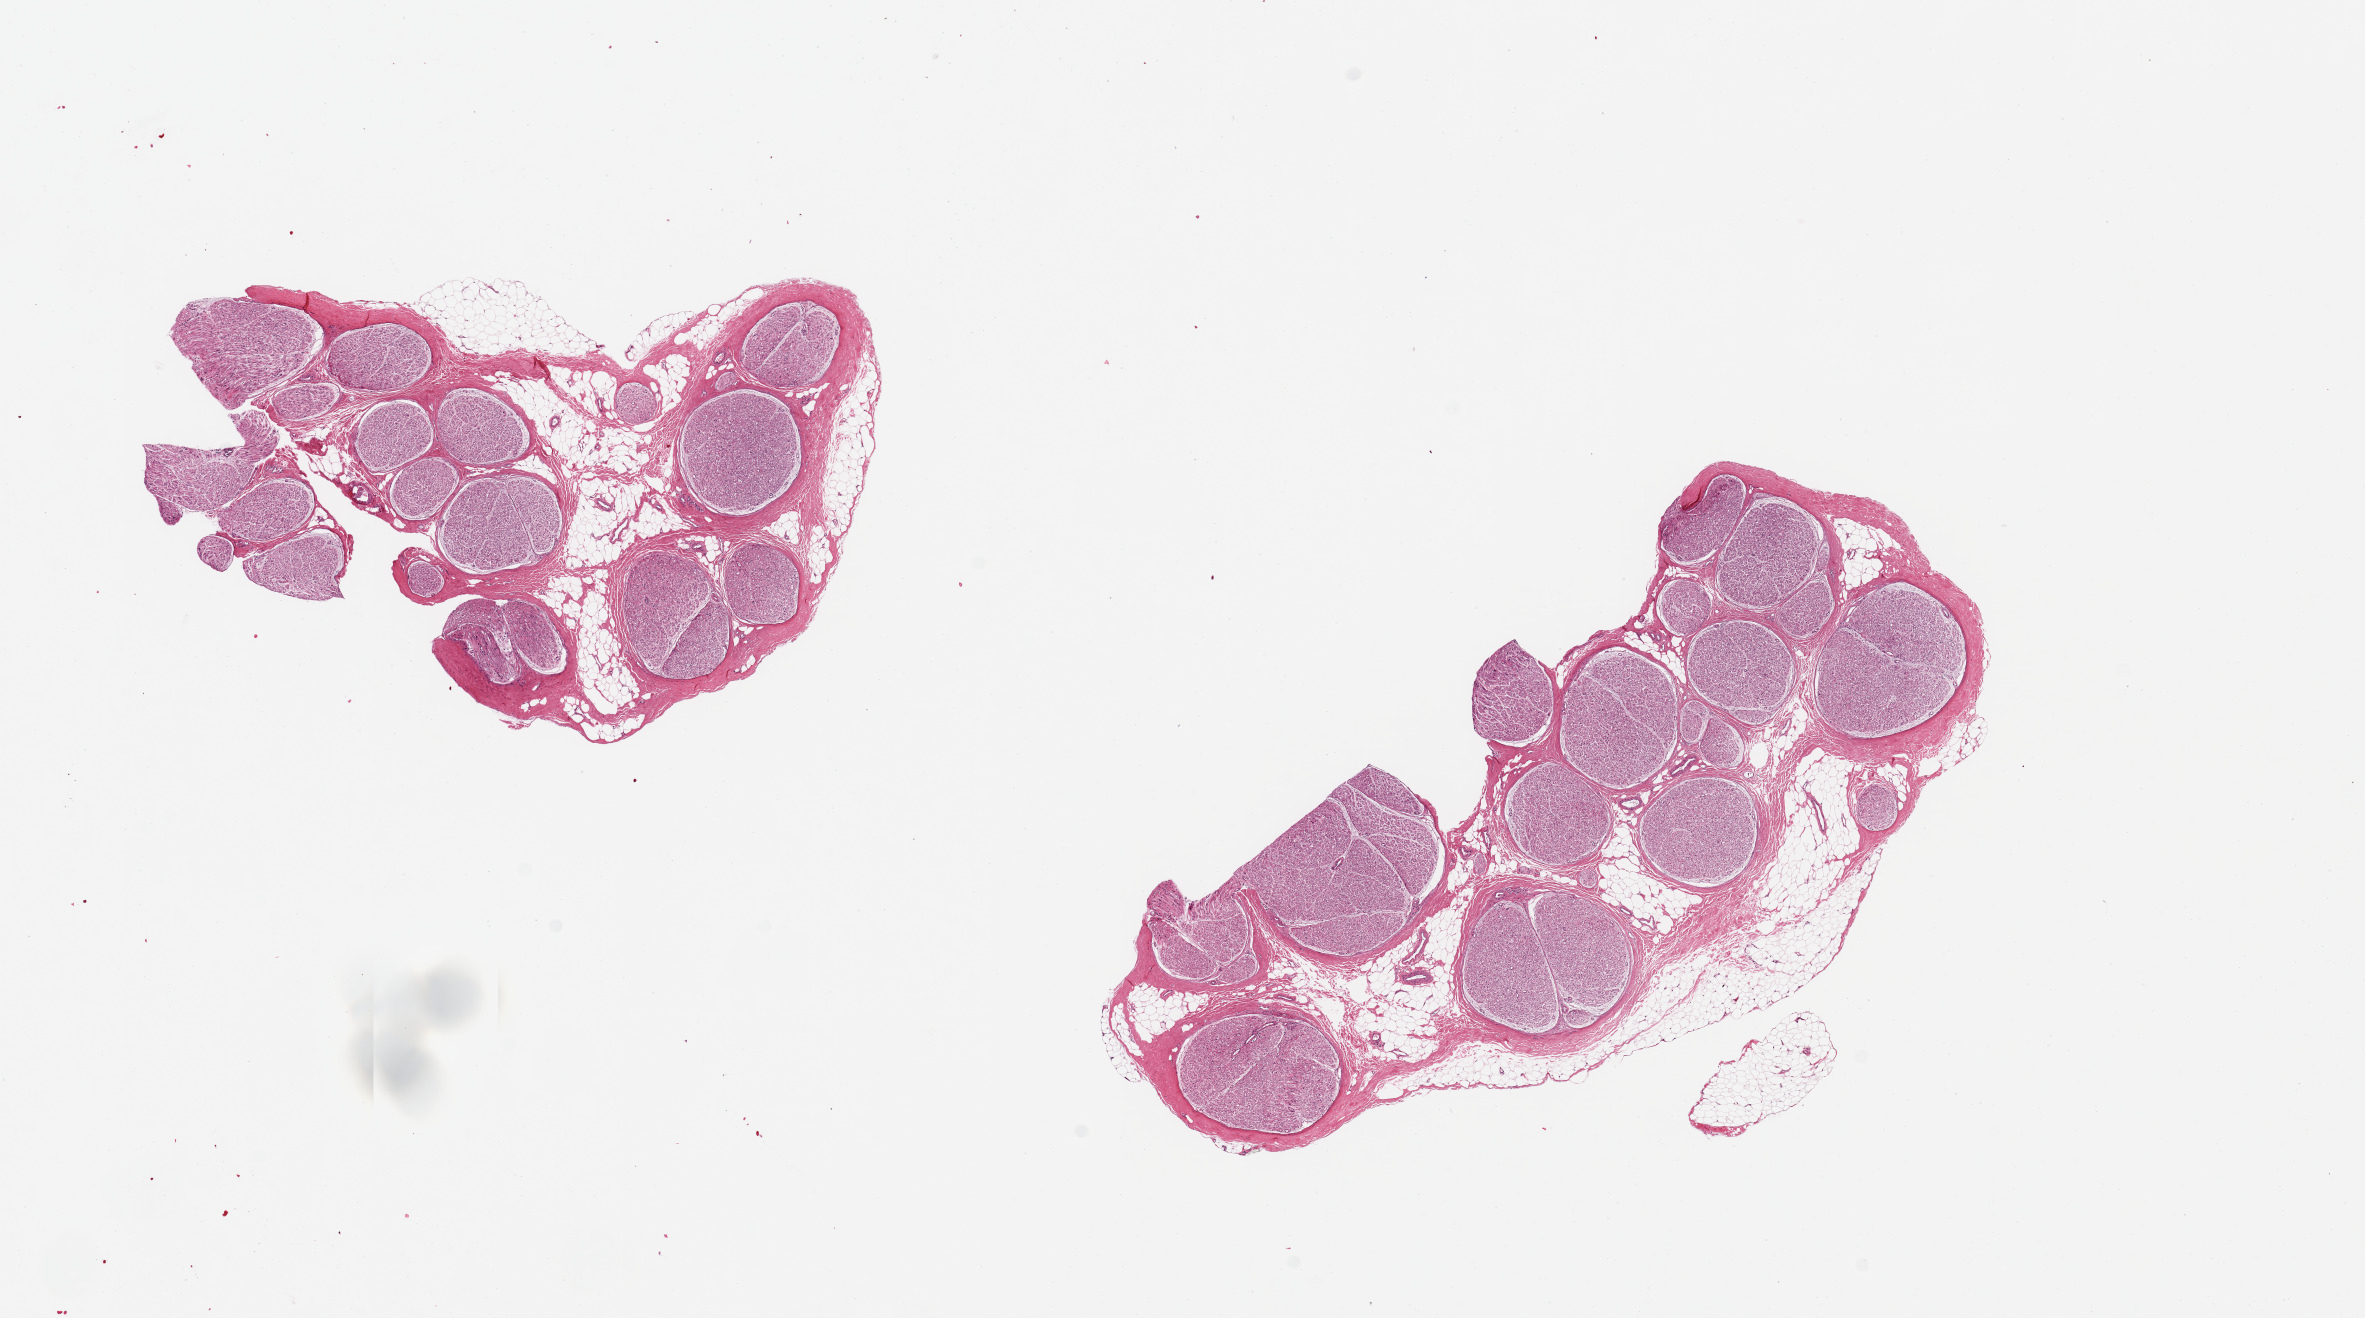
Digitized haematoxylin and eosin-stained section, shown as a low-resolution overview of the whole scanned area (about 18.7 x 10.4 mm); PAXgene-fixed, paraffin-embedded tissue; target tissue: tibial nerve; tissue donor sample. Male donor.
Pathologist's review note for this sample: 2 pieces ~7x4 mm, interstitial fat up to ~15-20% both aliquots.